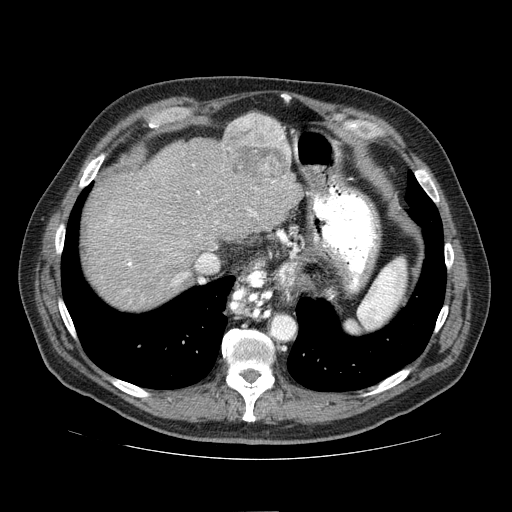
Contrast-enhanced abdominal CT (liver protocol), one axial slice; slice 60 of 81 in the series (ordered by position); 100 kVp; one of 2 acquisitions stored at this slice position; soft-tissue window (W 400 / L 40 HU); 2.5 mm slice thickness; 512 × 512 image matrix, field of view 400 × 400 mm. From the clinical record (not read from this slice): diagnosis: hepatocellular carcinoma (patient treated with transarterial chemoembolisation; whether this scan precedes or follows treatment is not stated here); TNM stage (as recorded): Stage-IIIA; Child-Pugh class: A; tumour differentiation: well differentiated; tumour nodularity: multinodular.
Annotated regions visible in this slice (semi-automatically segmented with operator editing):
- abdominal aorta: box from (x=272, y=316) to (x=295, y=339) px
- liver parenchyma outside the tumour (the mass and vessels are separate outlines, so this box may not span the whole liver): (x=84, y=118)–(x=300, y=310)
- mass: (x=220, y=111)–(x=291, y=184)
- liver vessels: (x=110, y=181)–(x=275, y=284)